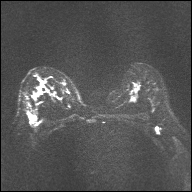
Breast MRI, one axial slice; diffusion-weighted series; image 2 of 4 stored at this slice position (different b-values; order by instance number); 1.5 T; 4 mm slice thickness; 192 × 192 image matrix, field of view 360 × 360 mm. Female patient.
Outlined on this slice (expert manual segmentation):
- tumour on diffusion-weighted imaging: bounding box <37,90,41,95> (left, top, right, bottom; pixels)